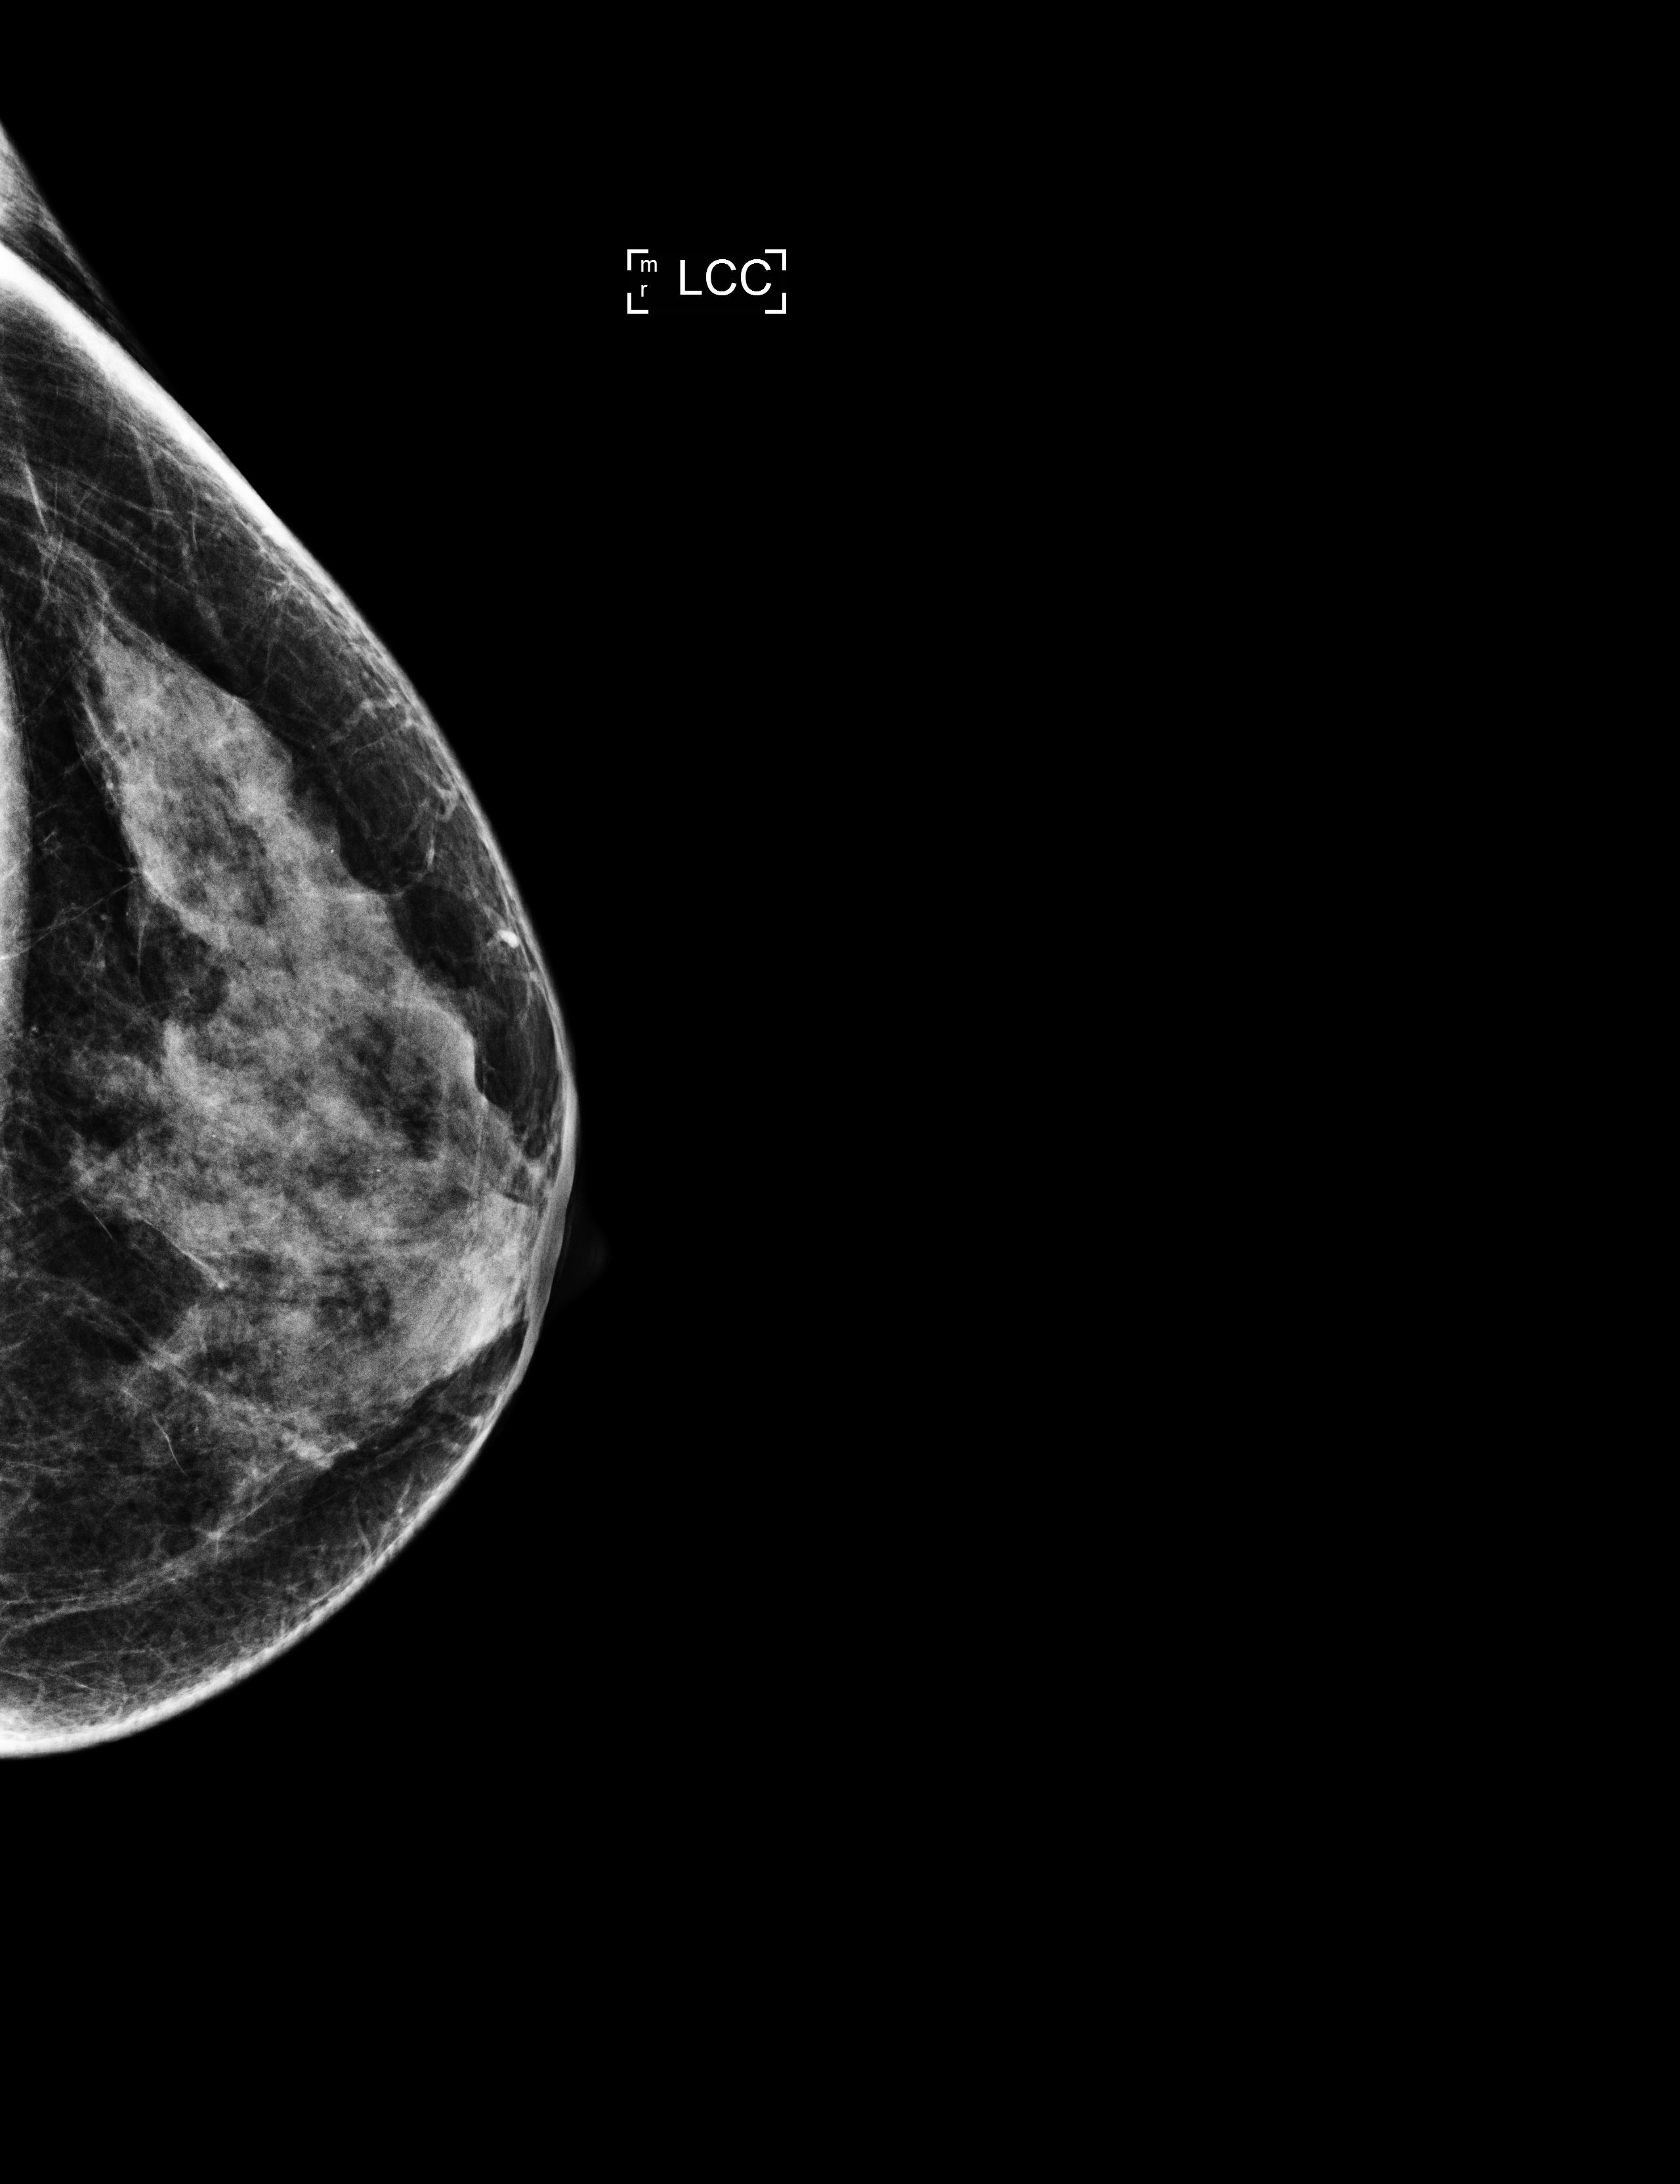
Screening examination, compressed breast thickness 38 mm, system: Selenia Dimensions. Patient aged 51 years (female).
Image type: full-field digital mammogram. Breast: left. Projection: CC view.